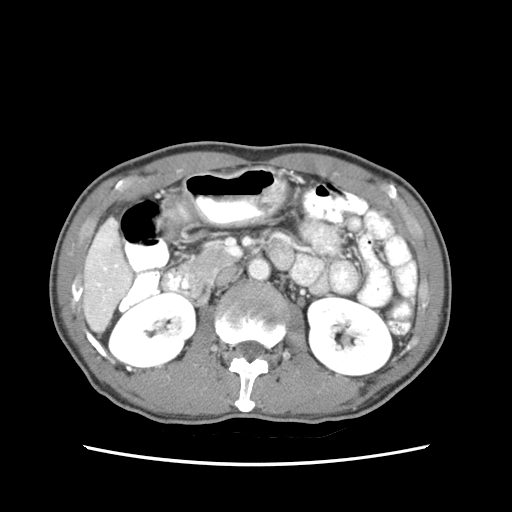
Contrast-enhanced abdominal CT (liver protocol), one axial slice. Slice 19 of 79 in the series (ordered by position). Reconstruction kernel STANDARD. 120 kVp. Soft-tissue window (W 400 / L 40 HU). 2.5 mm slice thickness. 512 × 512 image matrix, field of view 320 × 320 mm. Case-level facts recorded for this patient, not image findings: diagnosis: hepatocellular carcinoma (patient treated with transarterial chemoembolisation; whether this scan precedes or follows treatment is not stated here); TNM stage (as recorded): Stage-IIIB; Child-Pugh class: A.
Outlined on this slice (semi-automatic segmentation, software-assisted and operator-edited):
- liver parenchyma outside the tumour (the mass and vessels are separate outlines, so this box may not span the whole liver): bounding box <84,220,132,330> (left, top, right, bottom; pixels)
- liver vessels: <89,231,129,310>